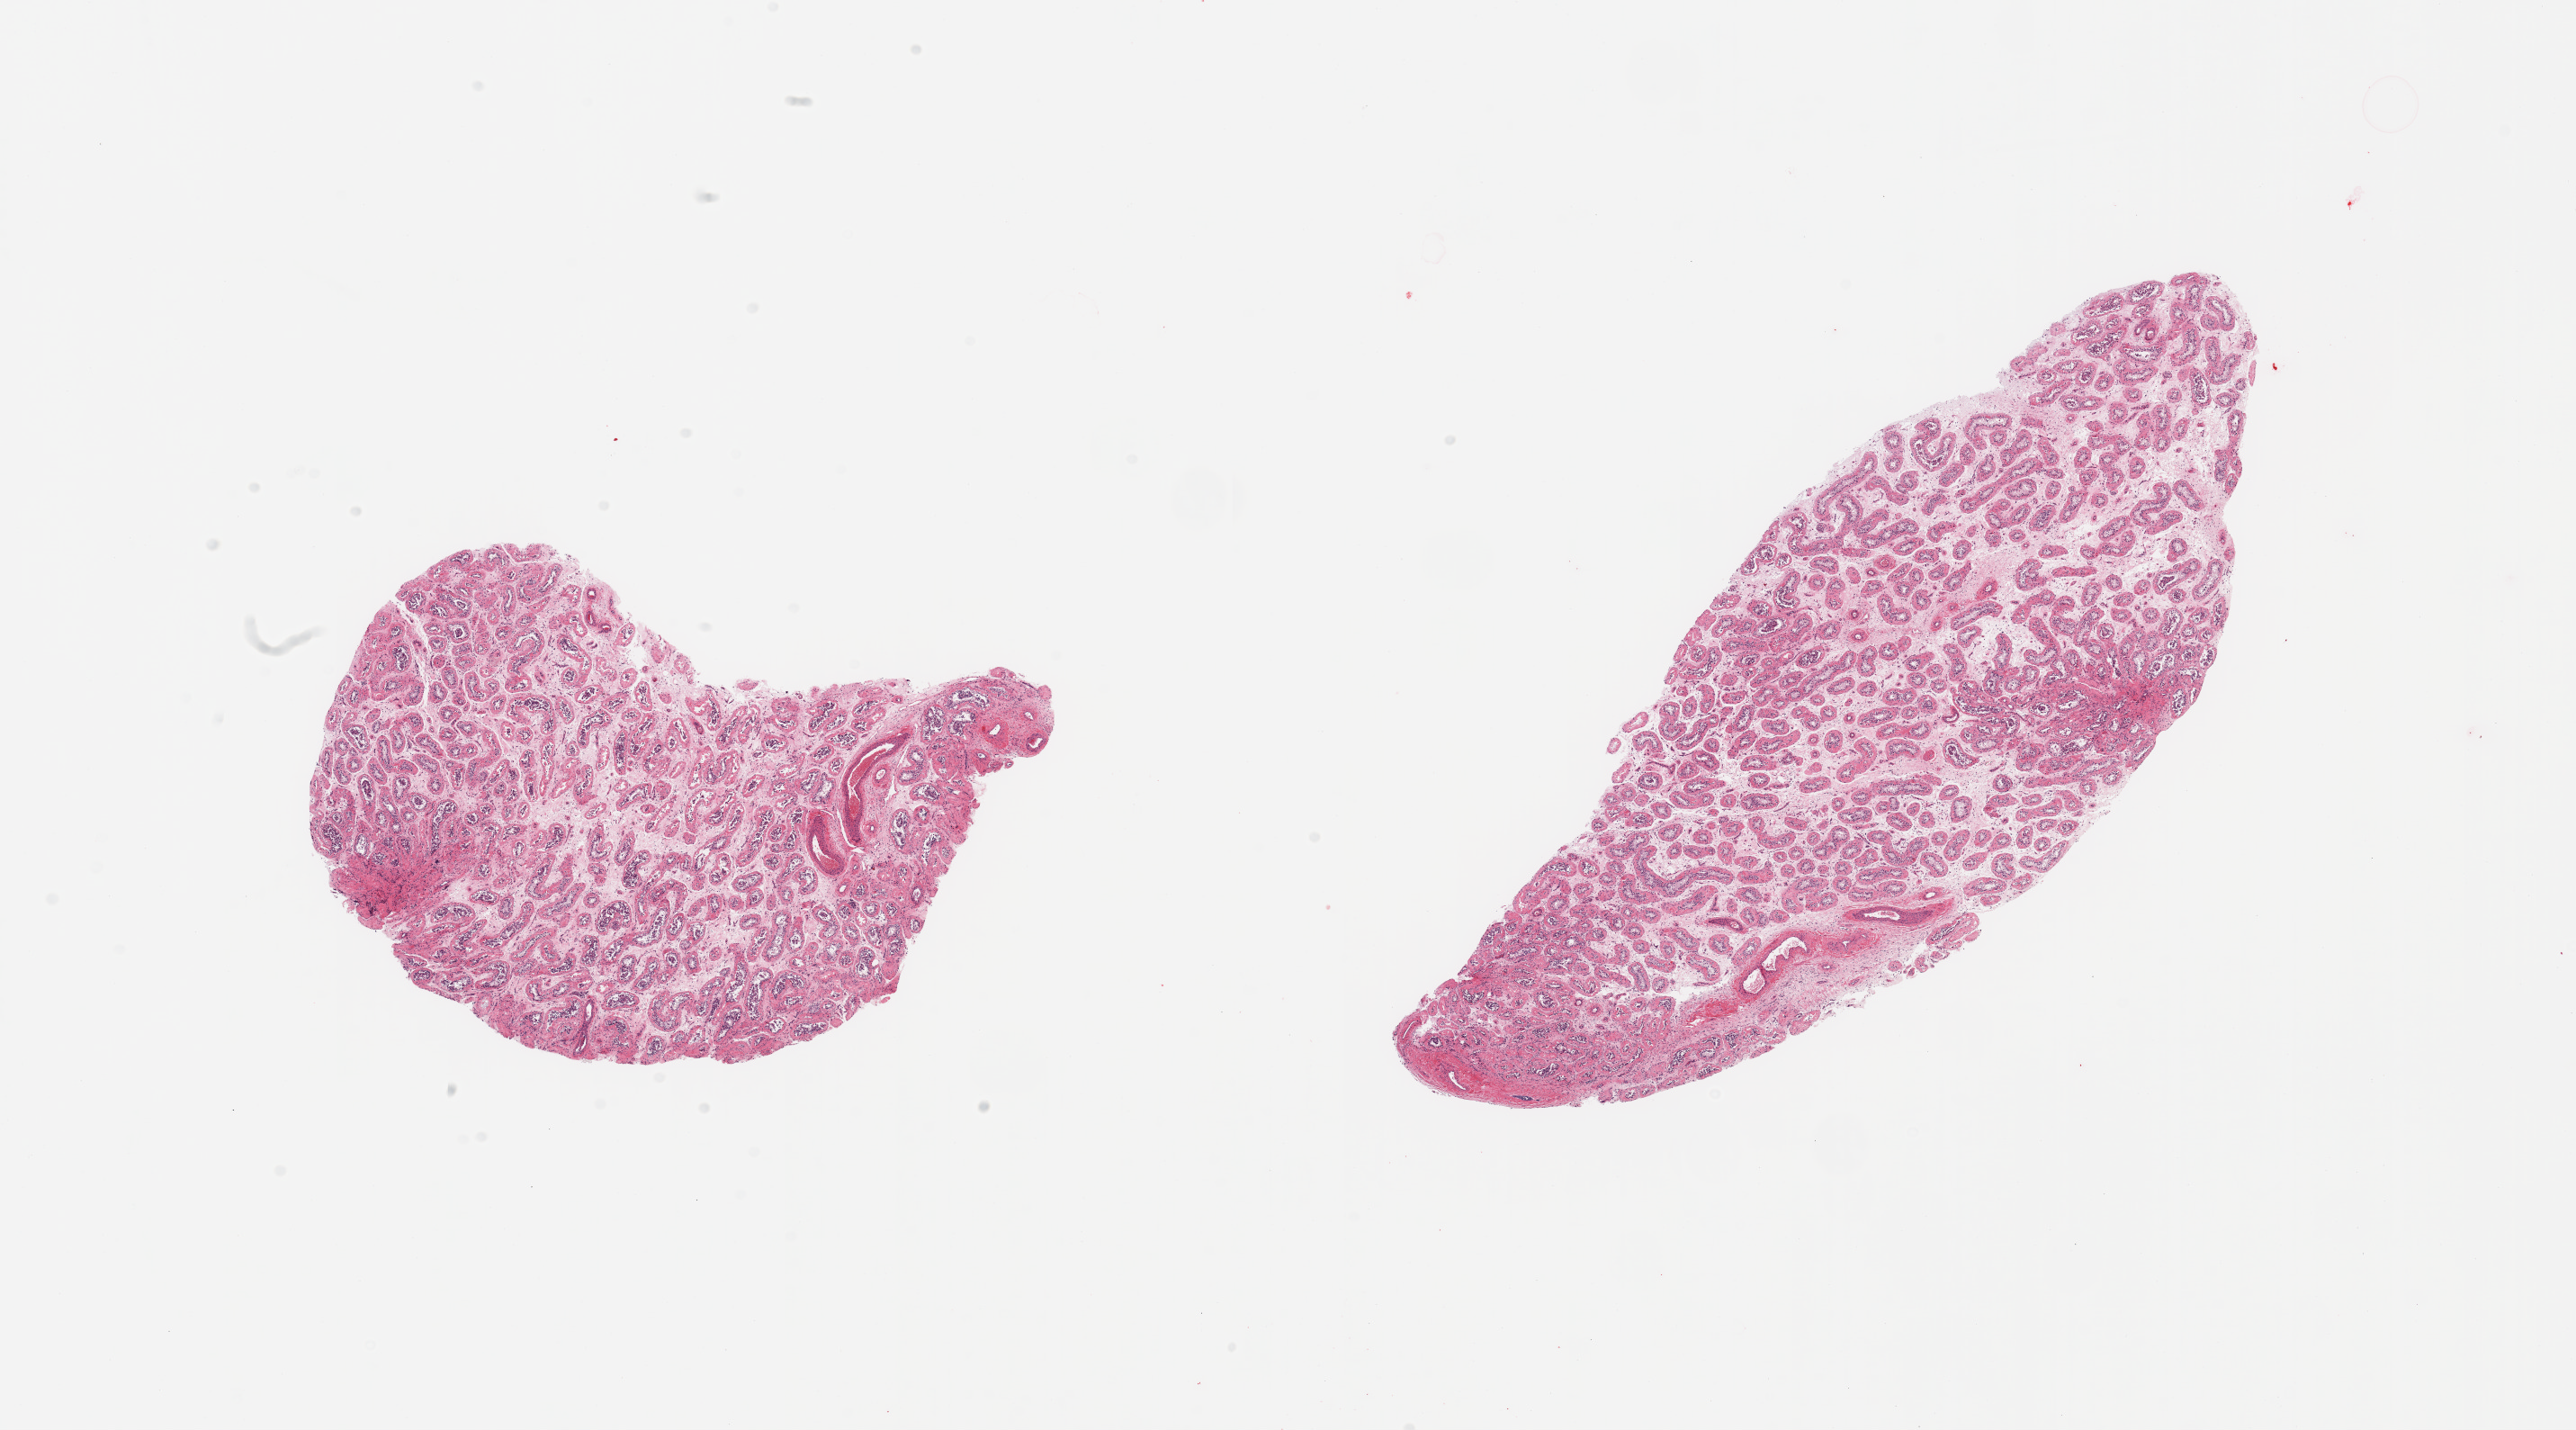
Whole-slide image, haematoxylin and eosin stain, brightfield, low-resolution overview of the scanned area, about 22.6 x 12.6 mm (from a 20x scan); PAXgene-fixed, paraffin-embedded tissue; target tissue: testis; donor tissue sample. Male donor.
Review note (as recorded): 2 pieces; greatly reduced spermatogenesis.